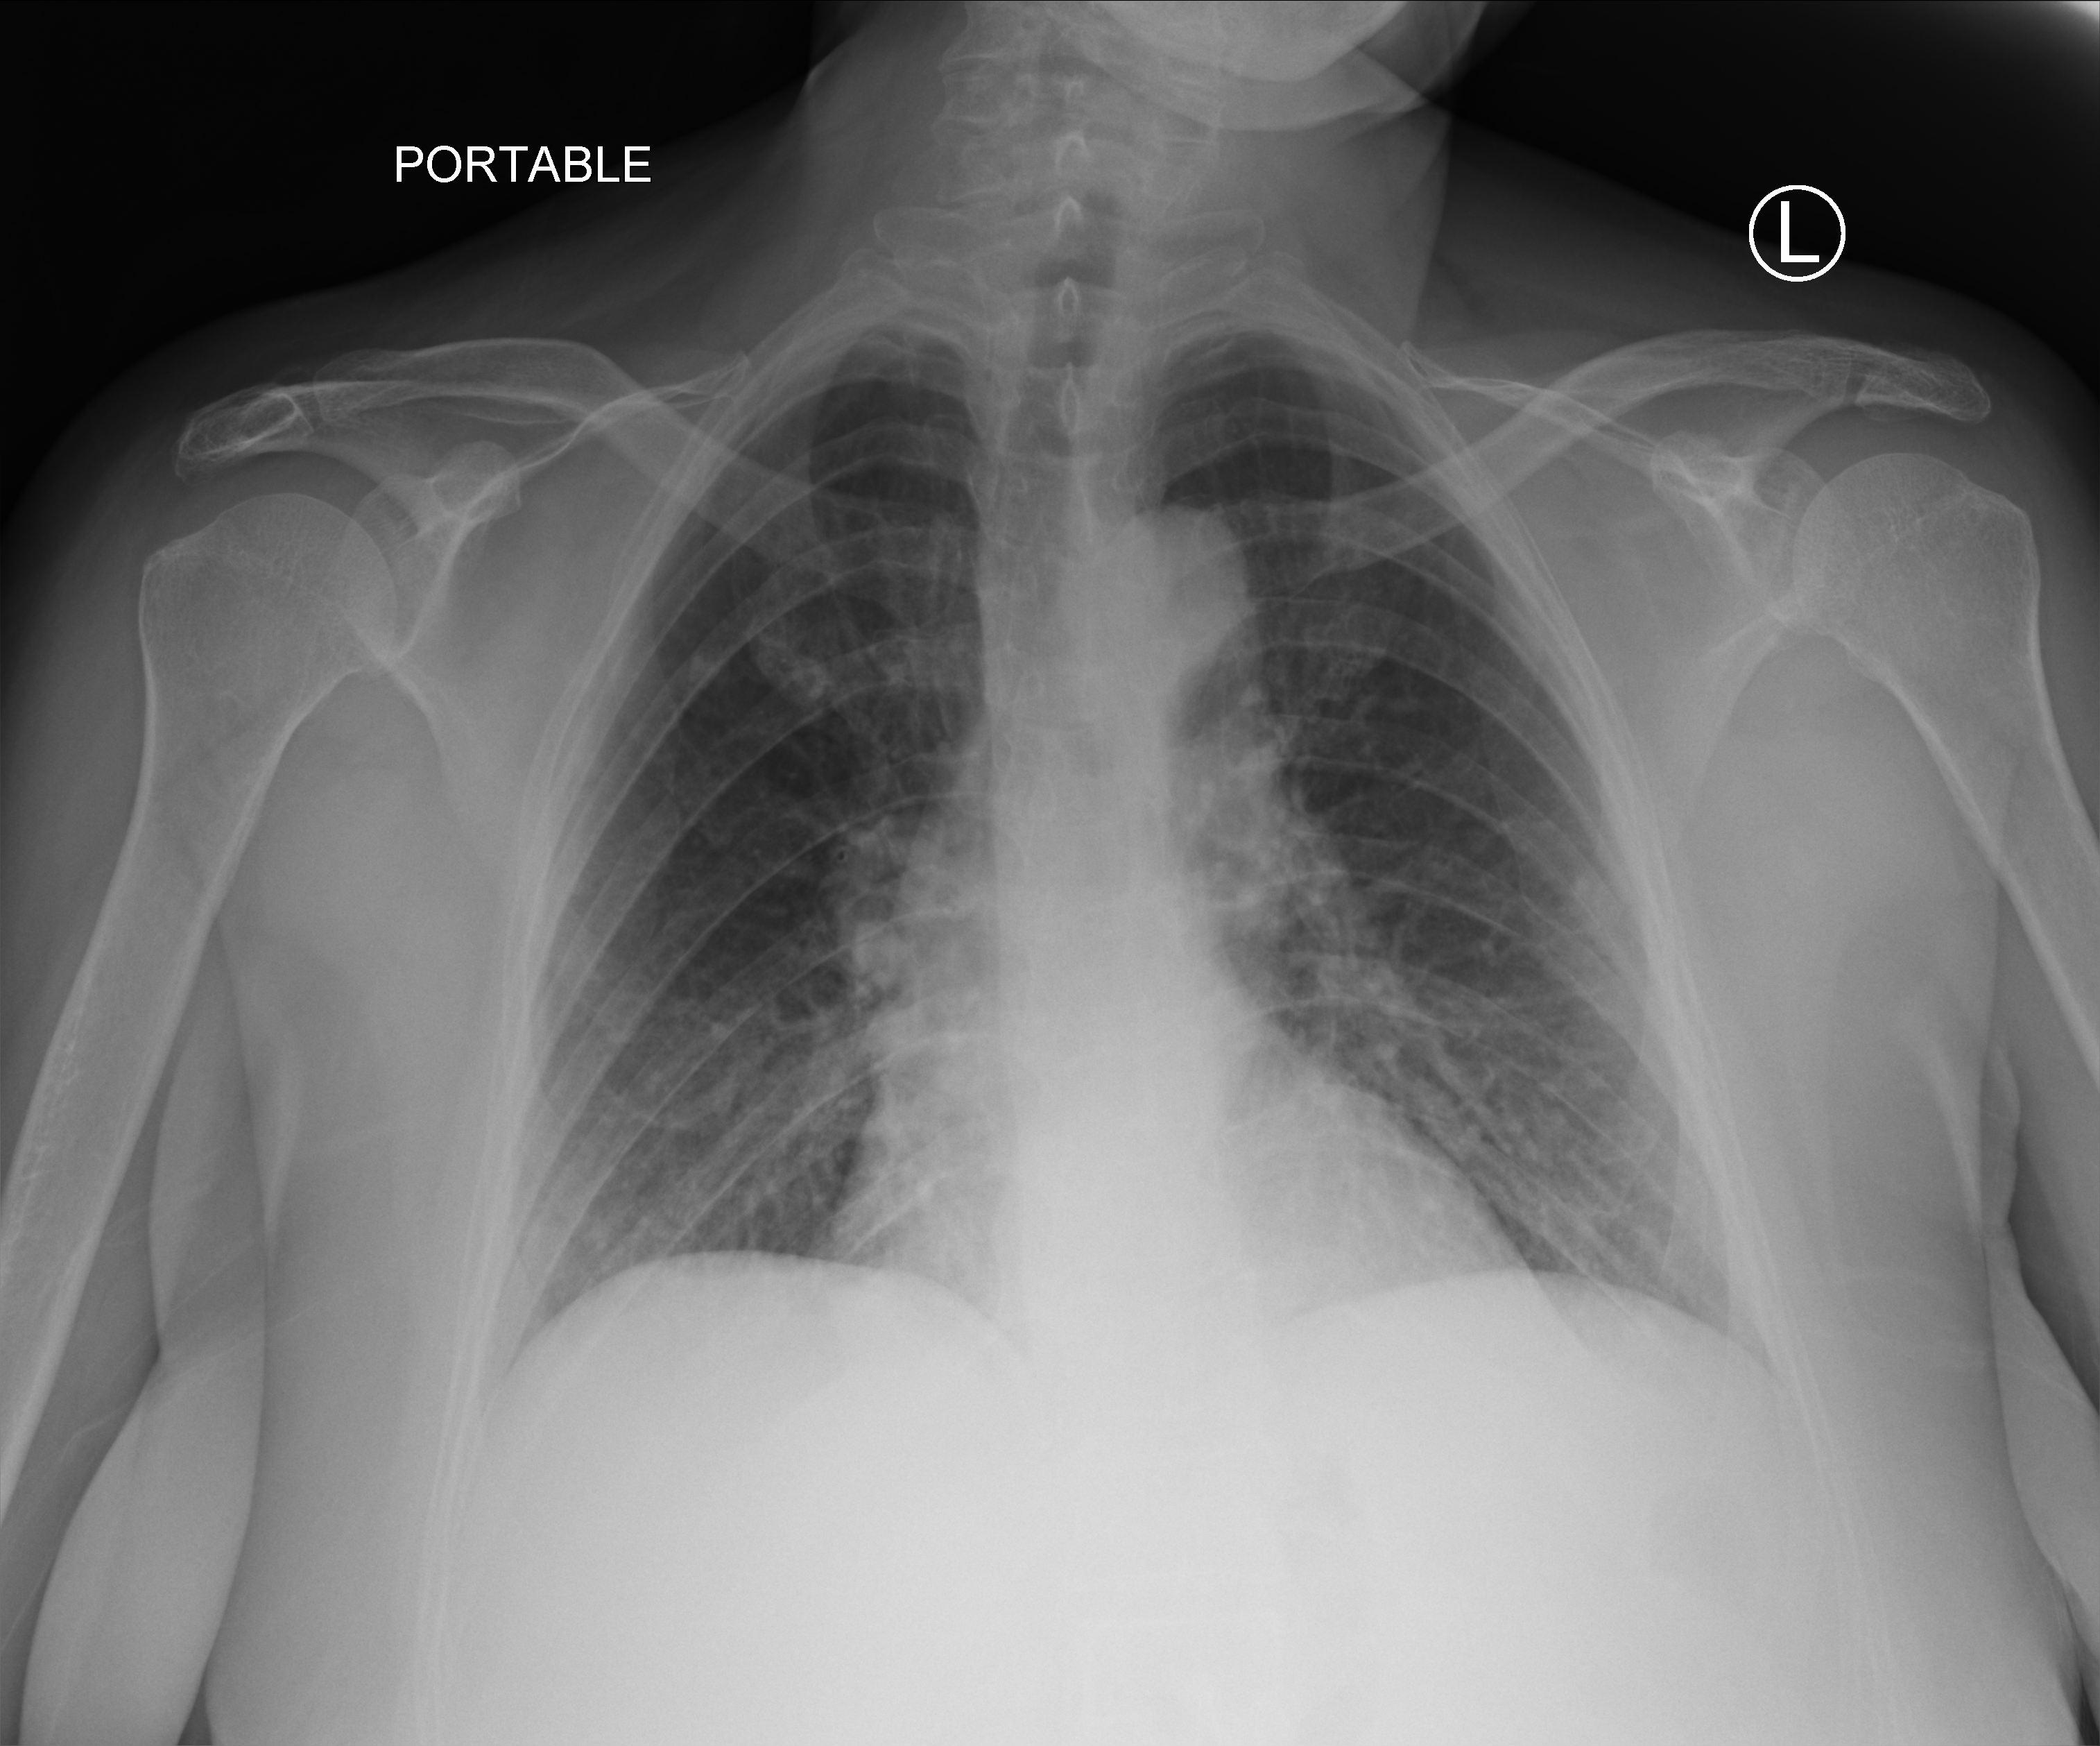
Chest X-ray (portable); anteroposterior (AP) projection. Female patient hospitalised with COVID-19, age 60–74 years.
From the hospital-stay record, not from the radiograph (when in the stay this image was taken is not recorded):
- admitted to intensive care during this hospital stay: no